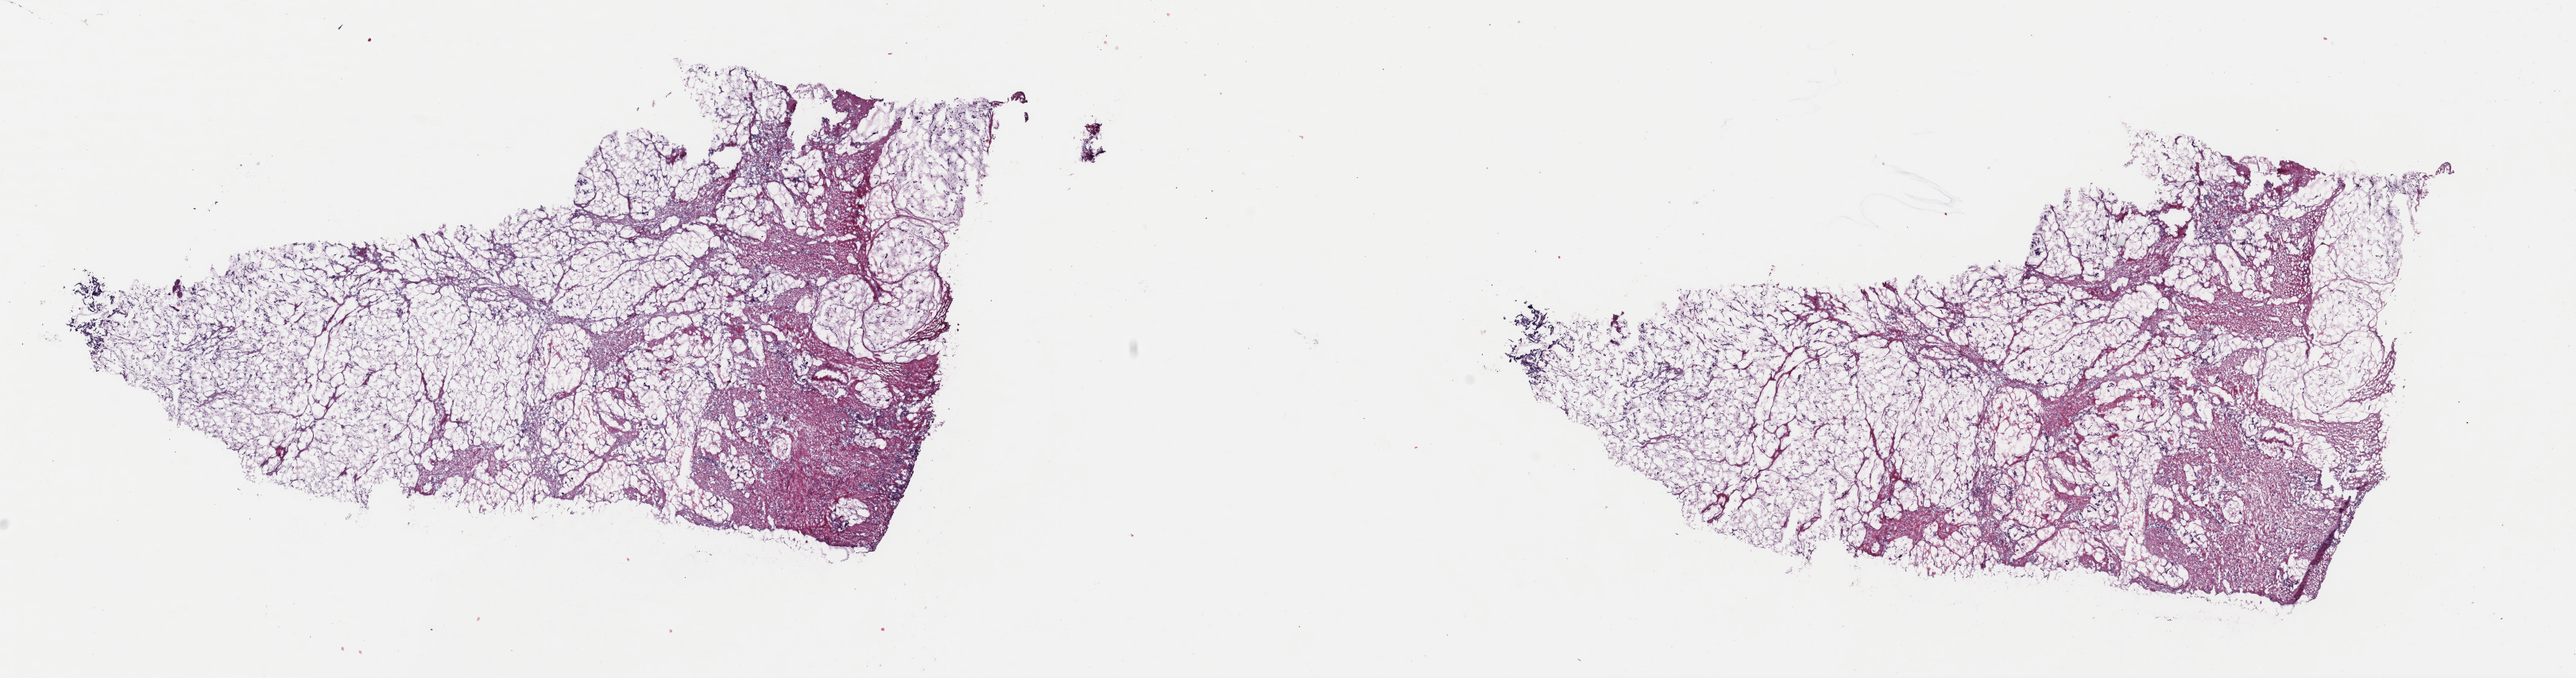
H&E whole-slide image, shown as a low-resolution overview of the whole scanned area (about 25.6 x 6.7 mm). Frozen section from the top of the tissue portion. Primary tumour sample from the stomach. Male, age 49 years at initial diagnosis. Histologic grade: G3 (poorly differentiated). Composition of this section per pathologist review: tumour cells 75%, tumour nuclei 100%, normal cells 0%, stromal cells 25%, necrosis 0%. Inflammatory infiltration, as recorded: lymphocyte infiltration 0%, monocyte infiltration 1%, neutrophil infiltration 0%.
* AJCC pathologic stage: IIB (7th edition)
* pathologic diagnosis: Mucinous adenocarcinoma